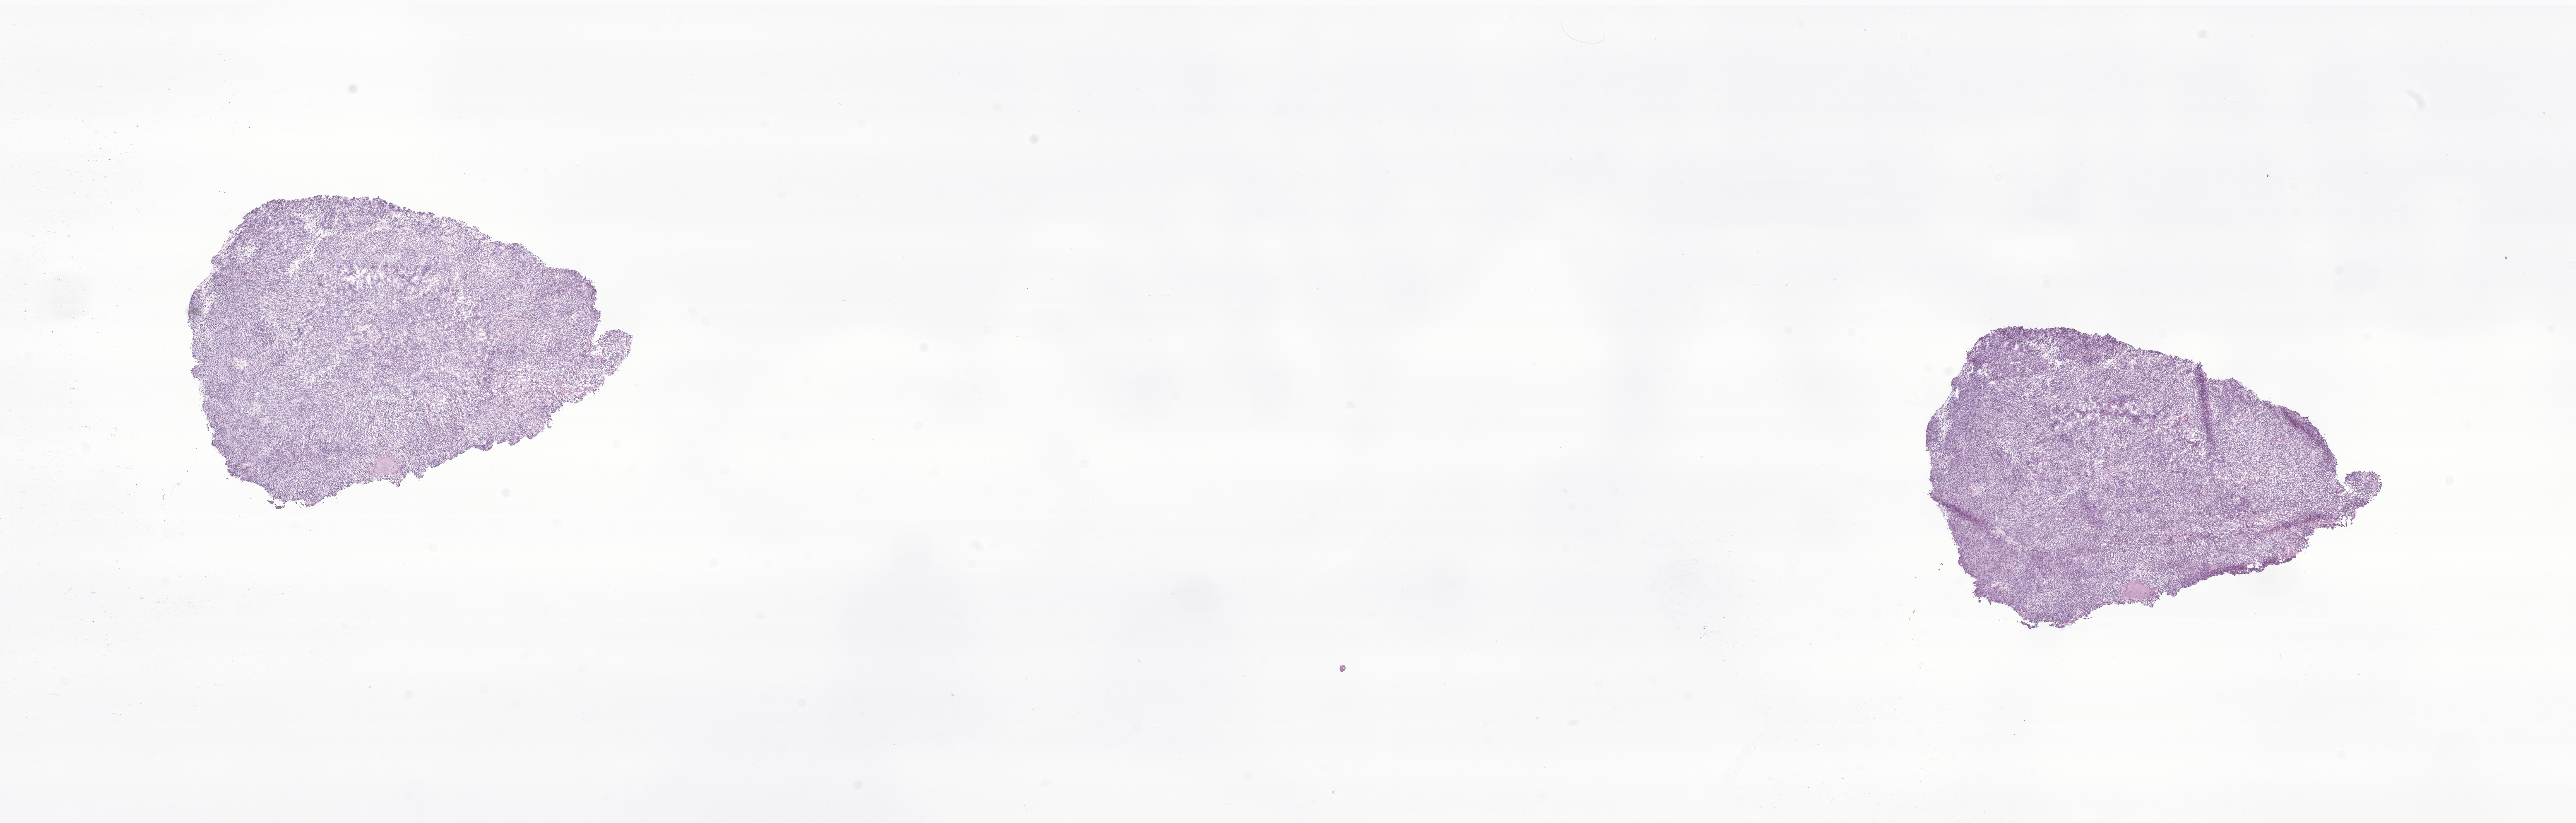
Whole-slide image, H&E stain of tumor tissue from the brain — low-resolution overview of the scanned area, about 26.2 x 8.4 mm. Frozen section. Male patient, age 85 months (7 years 1 month).
Recorded diagnosis: Medulloblastoma, NOS.